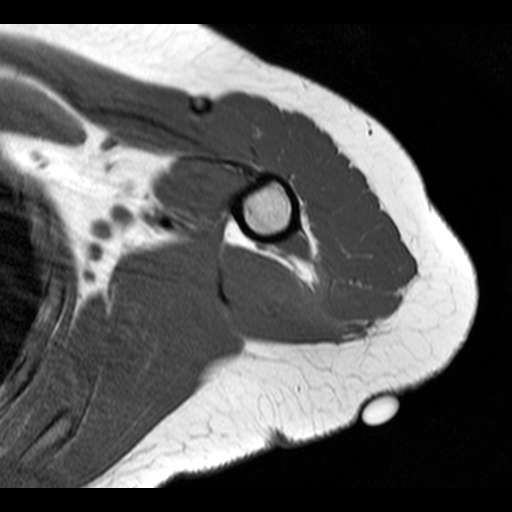
MRI of an extremity soft-tissue mass, one axial slice; position 4 of 20 along the scan axis; 512 × 512 image matrix. Female patient. Case-level facts recorded for this patient, not image findings: histological type: malignant fibrous histiocytoma; grade: low; site of the primary tumour: left arm.
Annotated regions visible in this slice (expert manual segmentation):
- gross tumour volume (mass): bounding box [x1, y1, x2, y2] px = [267, 264, 333, 330]